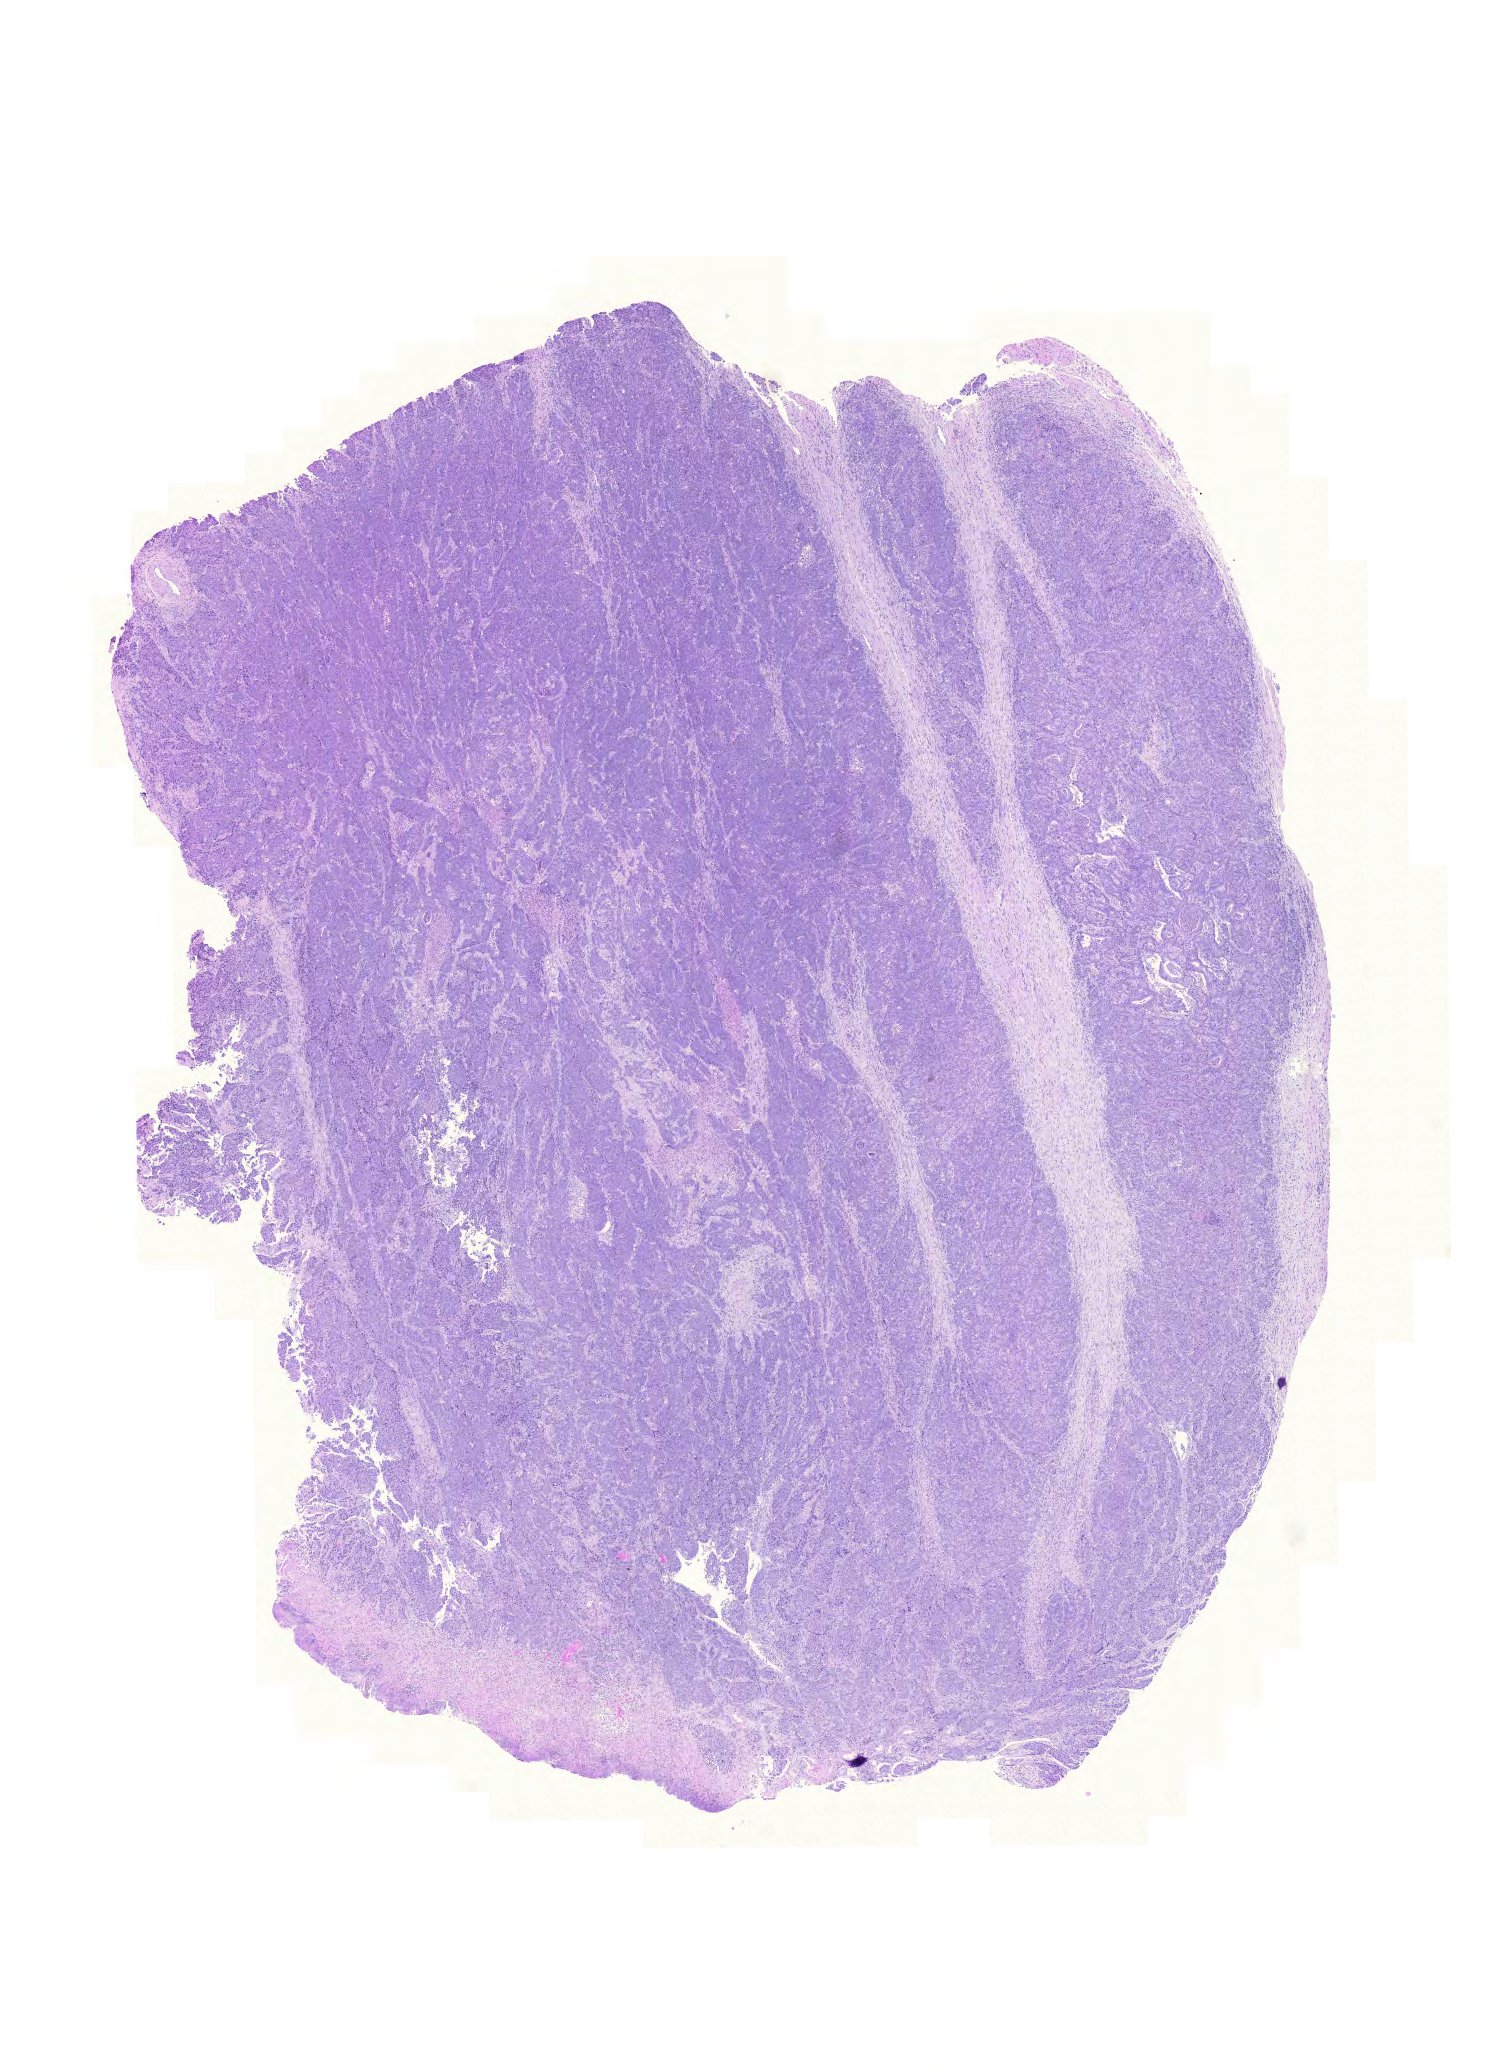
Whole-slide histology image, H&E, a low-resolution overview of the entire scanned area, about 11.2 x 15.4 mm (from a 20x scan), FFPE section, colon, primary tumour sample. Female patient; age at initial diagnosis 80 years.
Diagnosis: Adenocarcinoma, NOS (ascending colon).